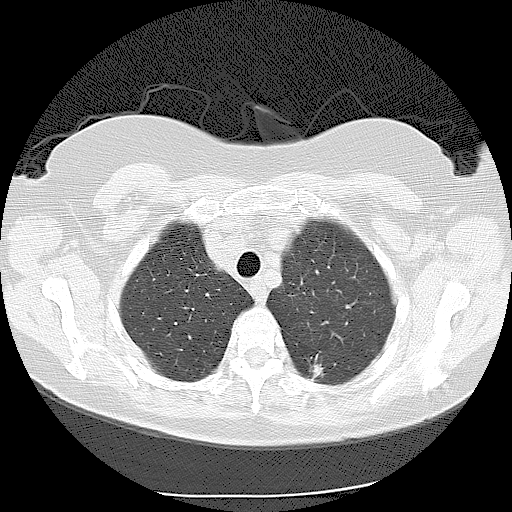
Axial slice from a low-dose chest CT screening exam; second screening round (one year after baseline); lung window (W 1500 / L -600 HU); 2.5 mm slice thickness; lung (sharp) reconstruction kernel (LUNG); slice 24 of 116 in the series. Female, age 56 years at enrolment. Current smoker at enrolment.
Lesion marked by an expert reader, box from (x=290, y=346) to (x=343, y=391) px. Reader record for this screening exam (exam-level; its link to the box is not recorded): non-calcified nodule or mass ≥4 mm, left lower lobe, 9 × 9 mm, spiculated (stellate) margins, soft tissue attenuation, pre-existing on the prior screen: yes; interval growth: yes. Official screen result: positive, other.